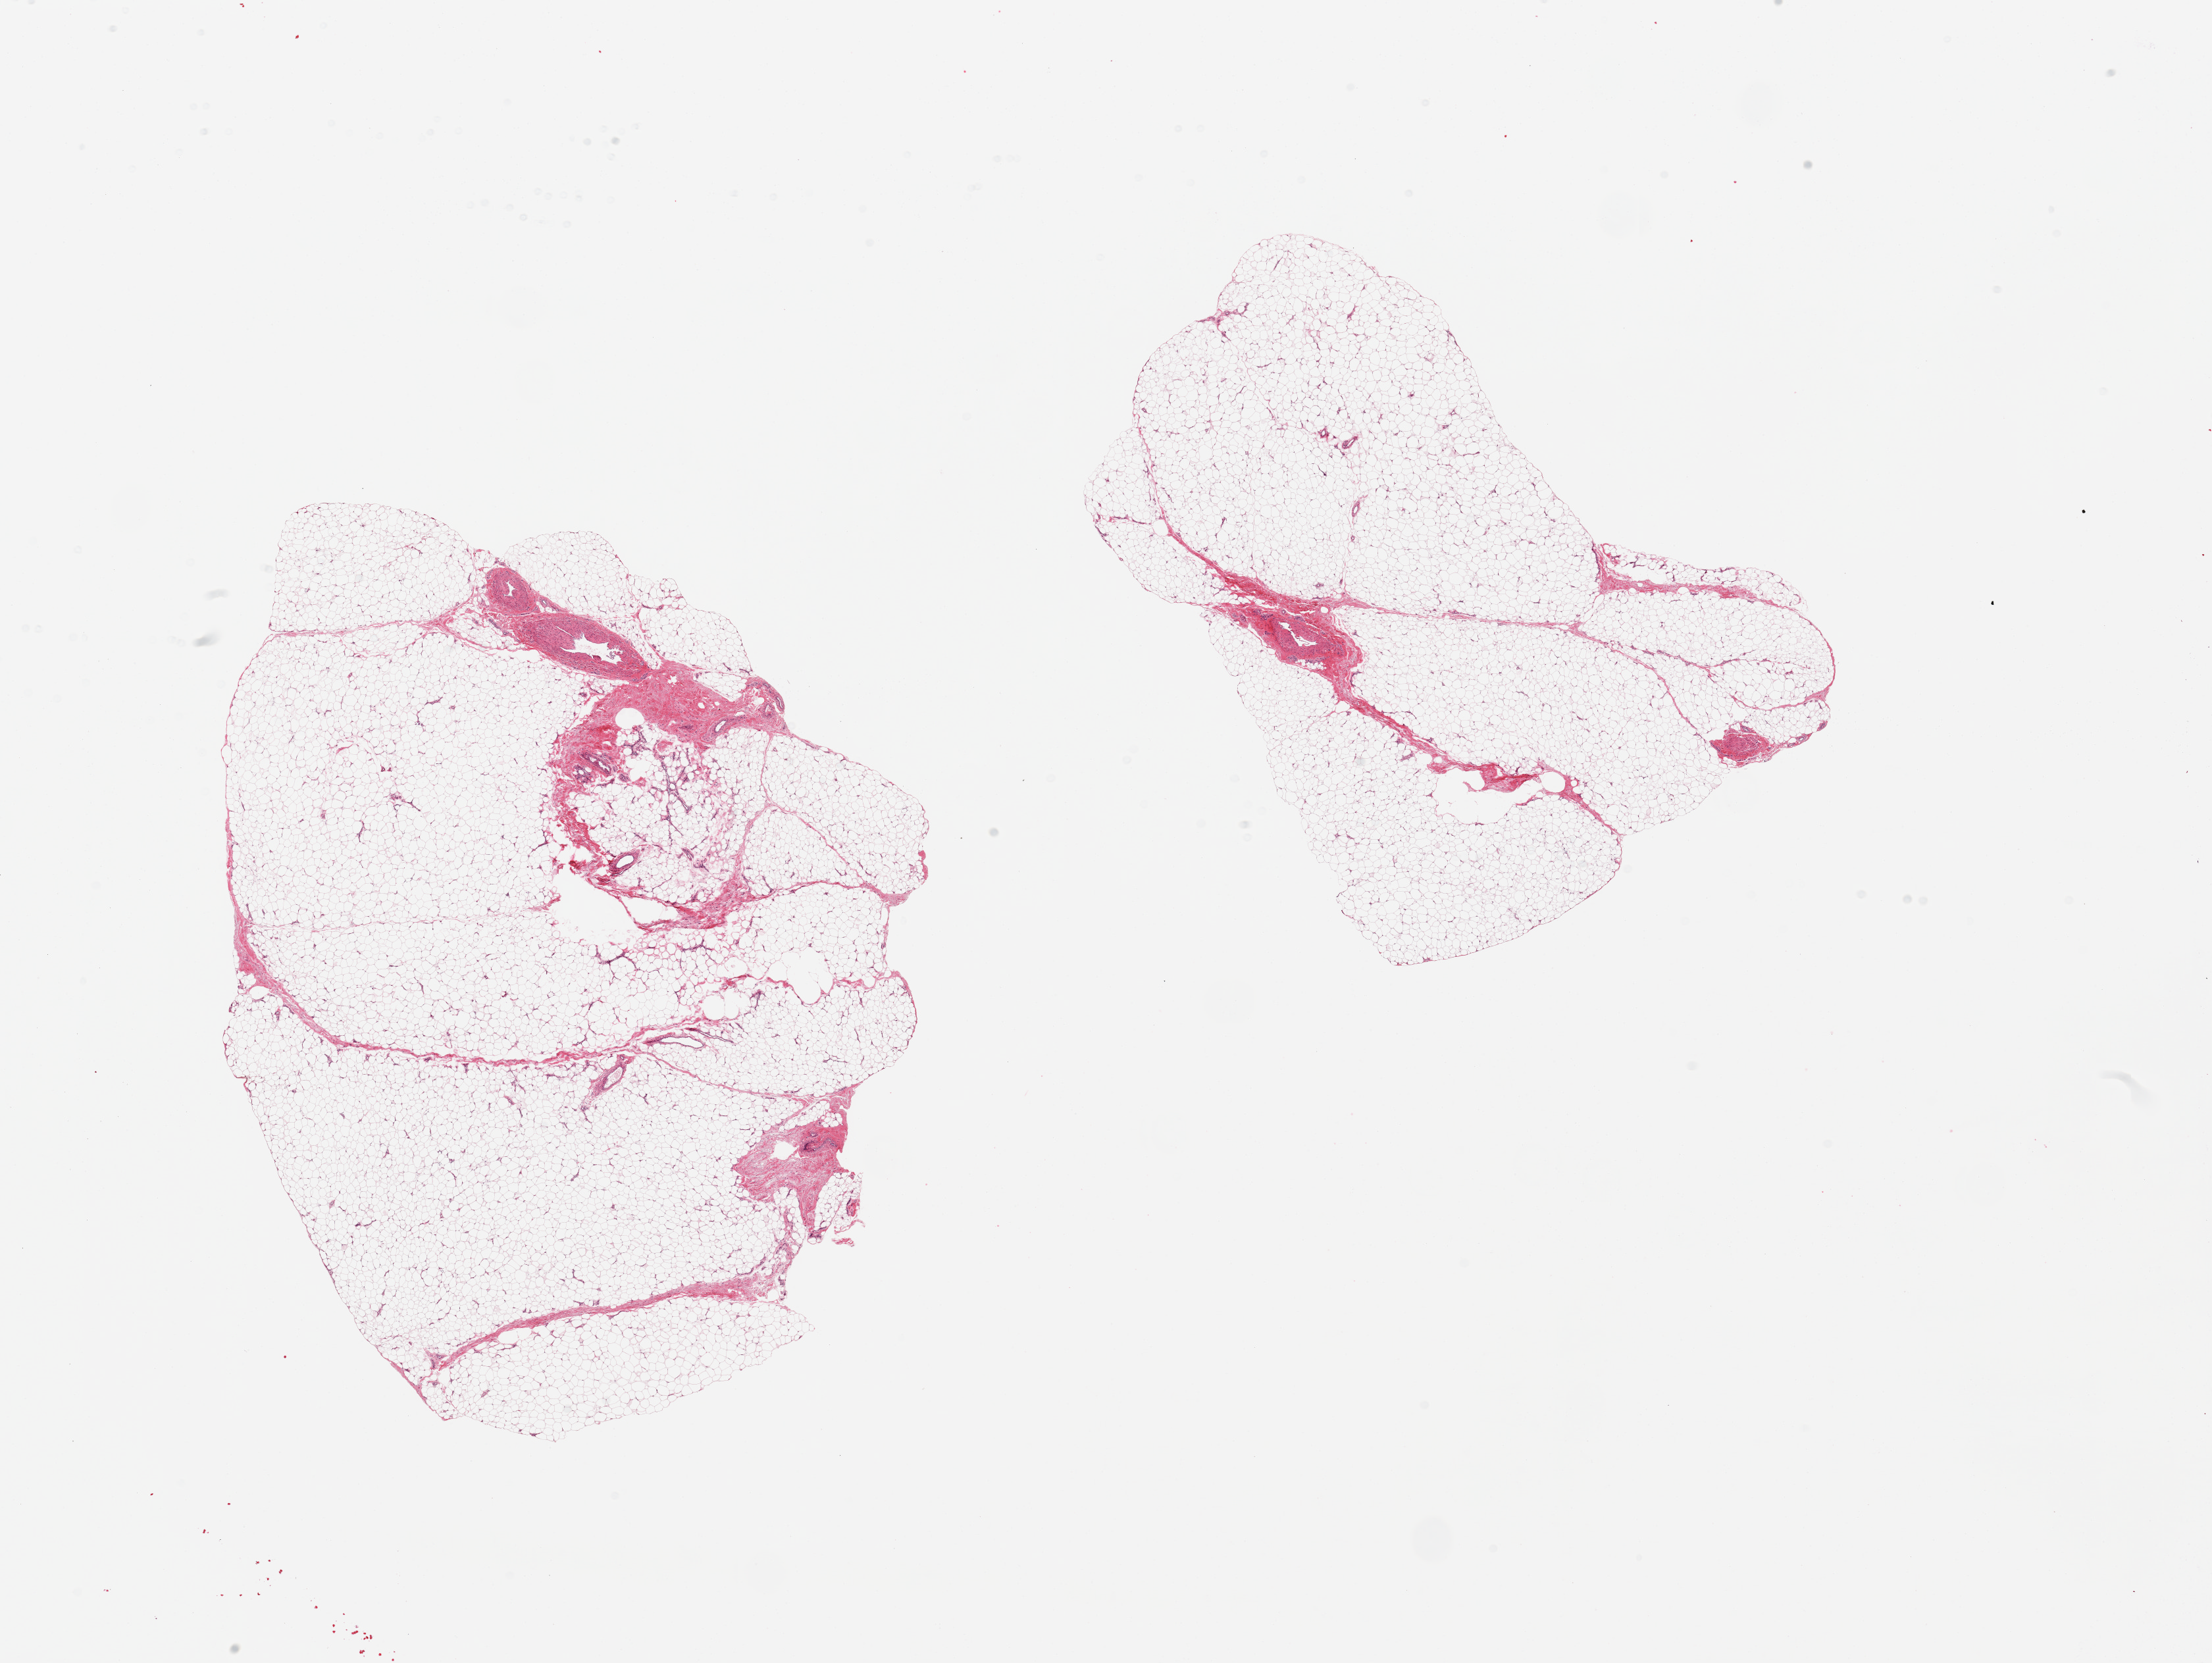
Hematoxylin and eosin (H&E) whole-slide image, a low-resolution overview of the entire scanned area, about 26.6 x 20.0 mm. PAXgene-fixed paraffin-embedded (PFPE) section. Sampled site (target tissue): adipose tissue. Tissue donor sample. Male donor.
* review note (as recorded): 2 pieces, 10-15% fascia